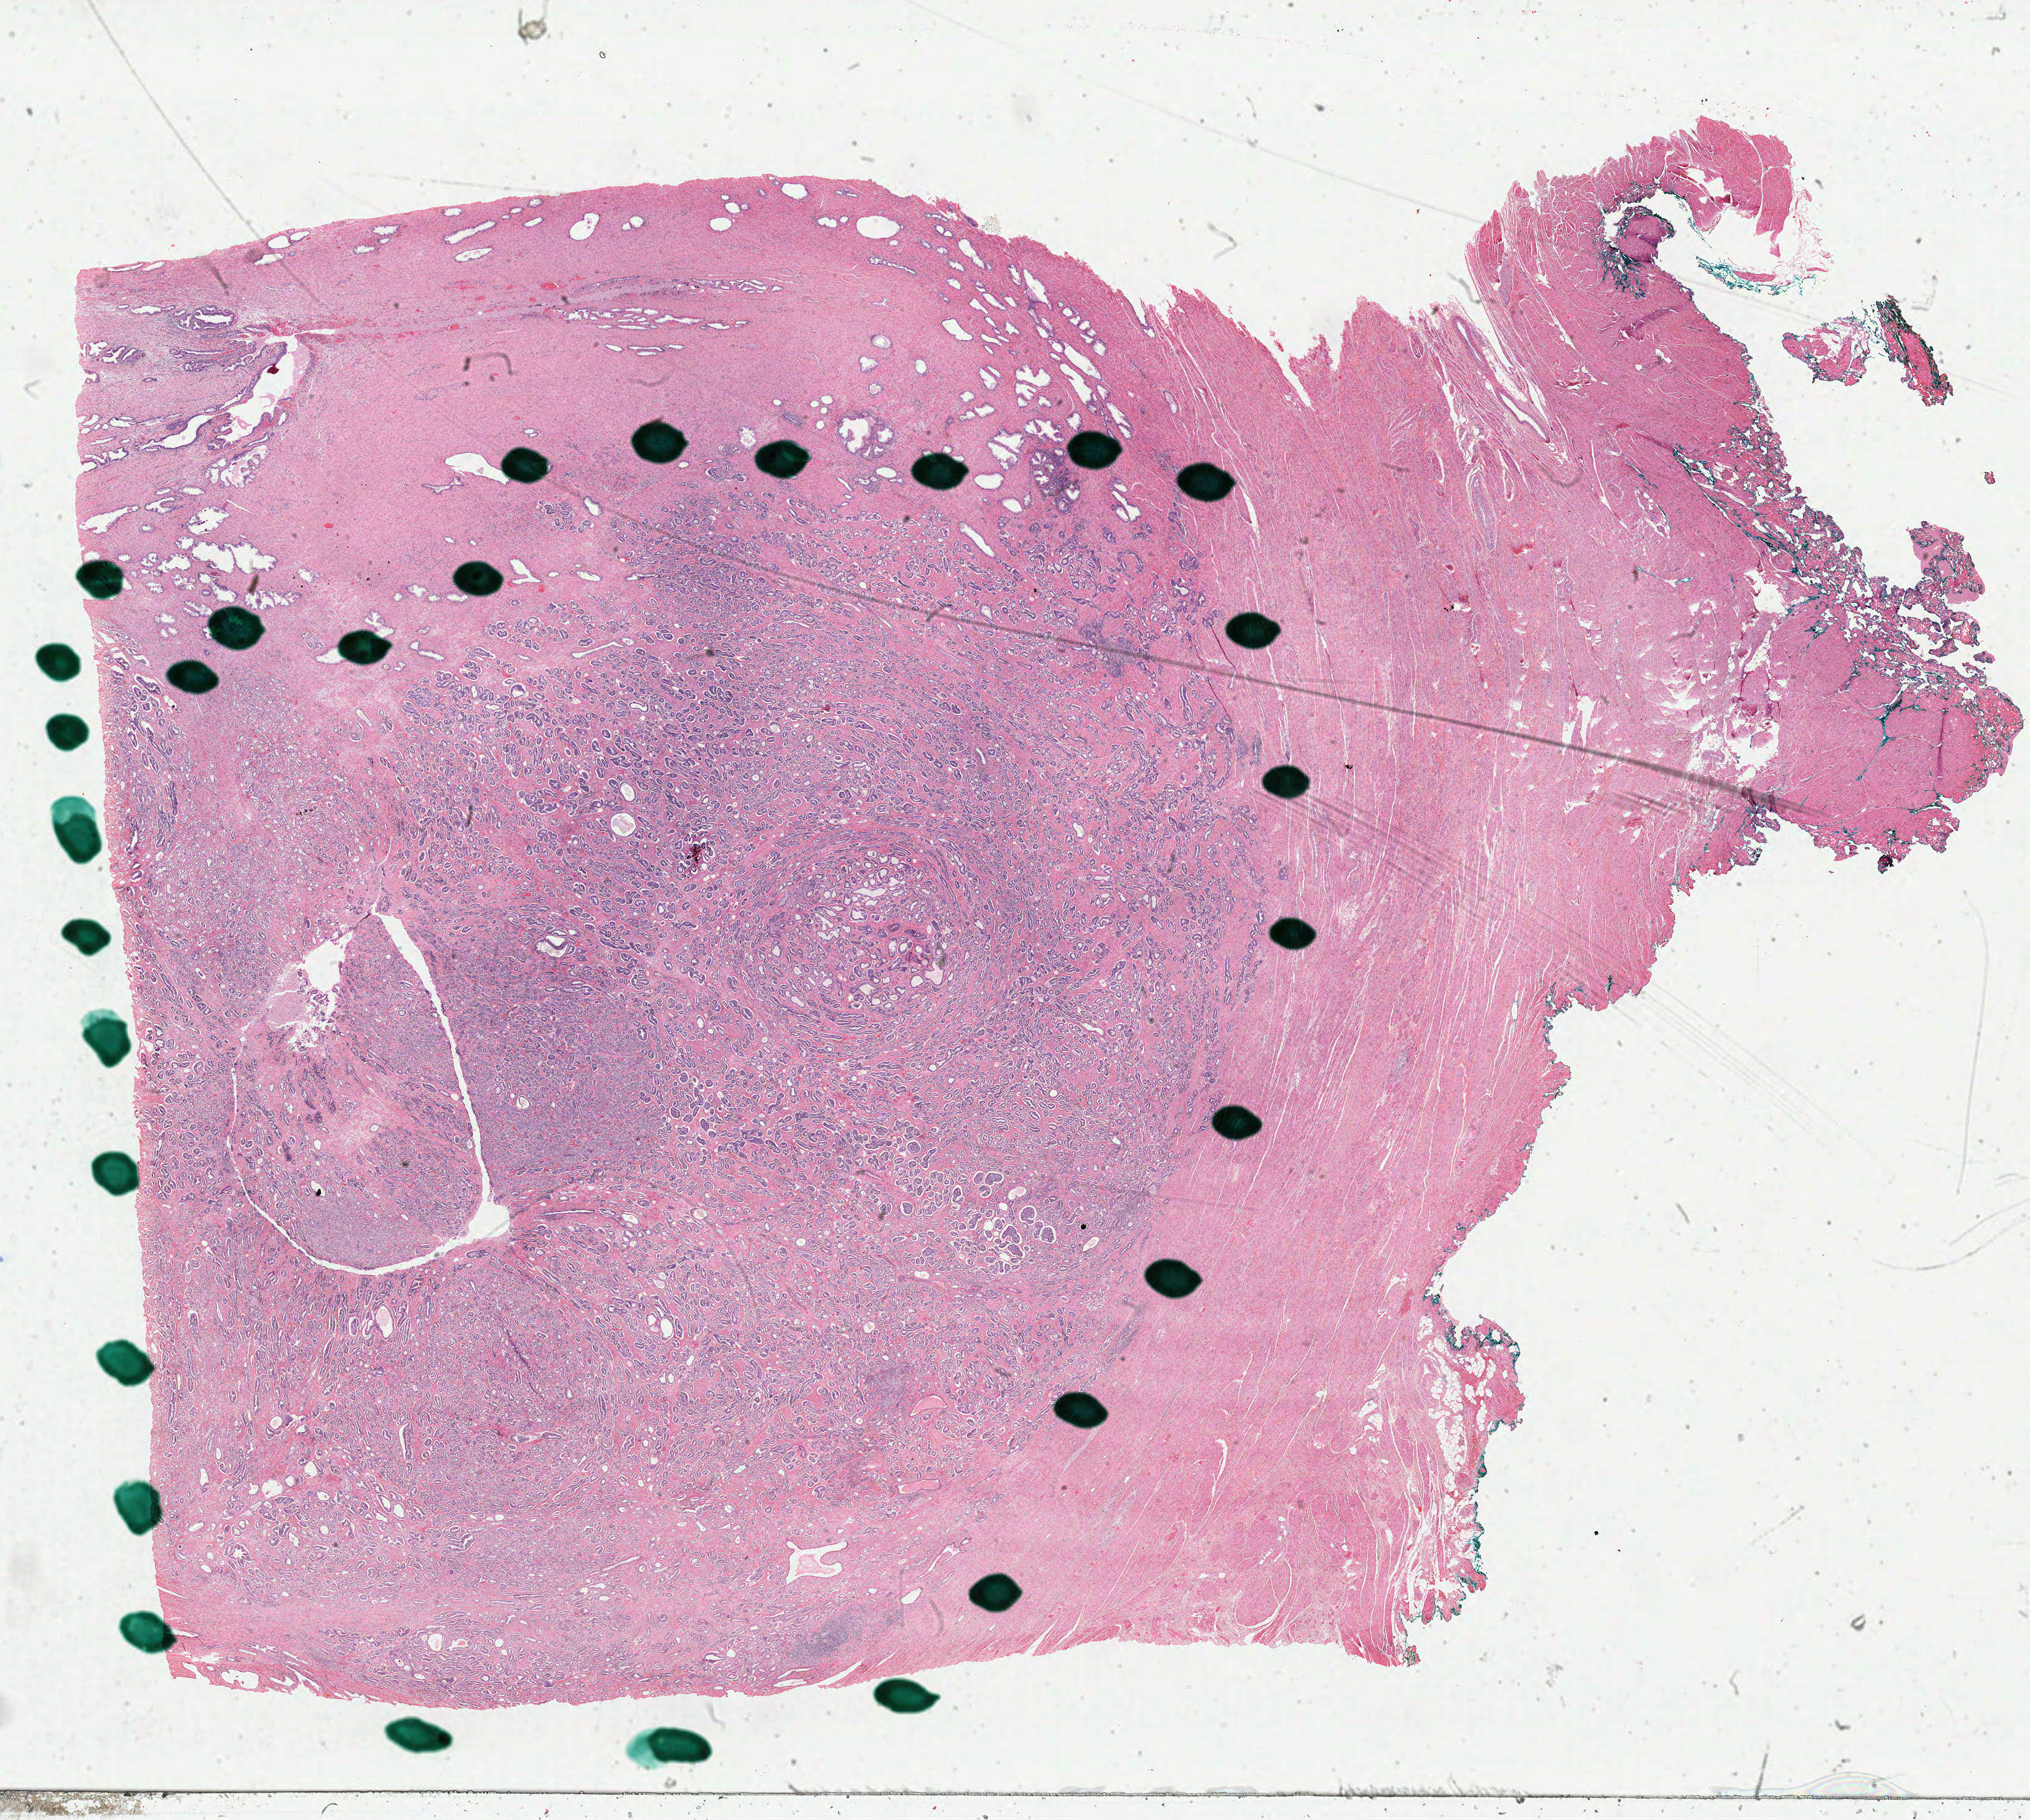
Digitized Hematoxylin and eosin (H&E) stained tissue section (whole slide) — low-resolution overview of the scanned area, about 26.1 x 23.4 mm (acquisition: 40x scan); formalin-fixed paraffin-embedded (FFPE) diagnostic section; sample: primary tumour, prostate. Male, age 54 years at initial diagnosis. Gleason score: 7 (3+4).
• histologic diagnosis: Adenocarcinoma, NOS